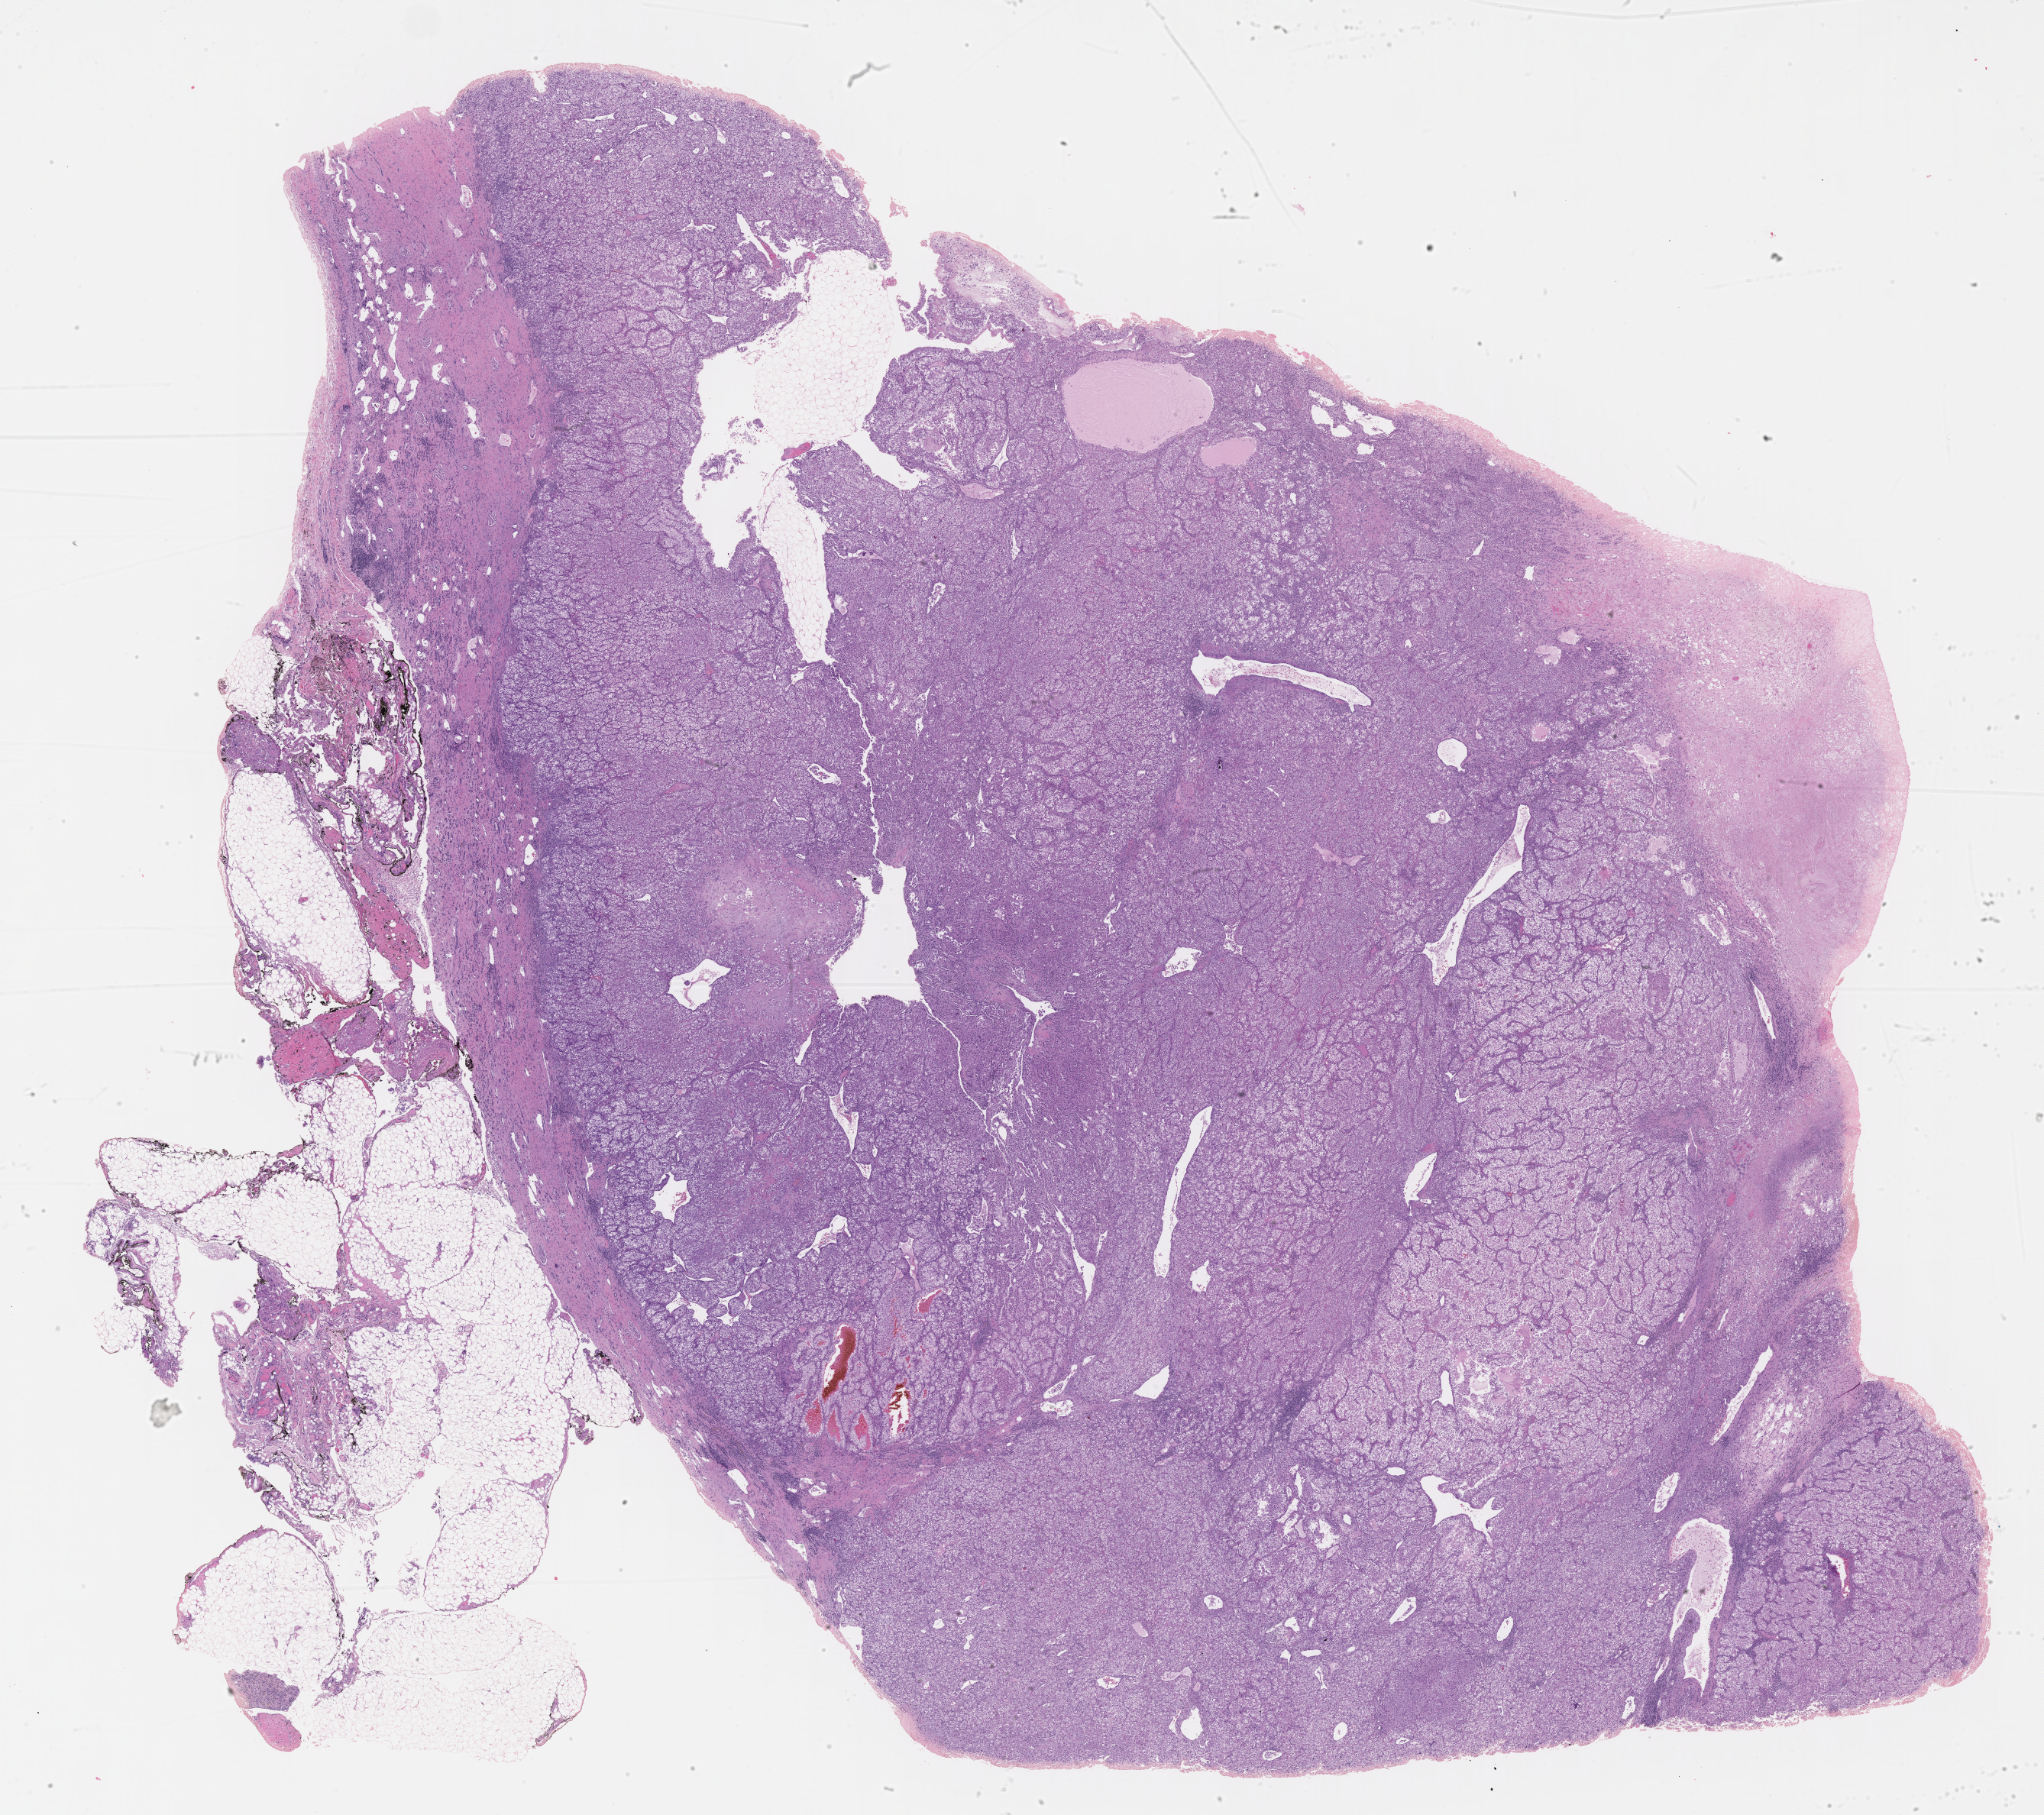
Digitized H&E-stained tissue section (whole slide) — shown as a low-resolution overview of the whole scanned area (about 21.6 x 19.2 mm); formalin-fixed paraffin-embedded (FFPE) diagnostic section; sample: primary tumour, kidney. Male, age 59 years at initial diagnosis. Histologic grade: G4 (undifferentiated).
AJCC pathologic stage: IV. Histologic diagnosis: Clear cell adenocarcinoma, NOS.